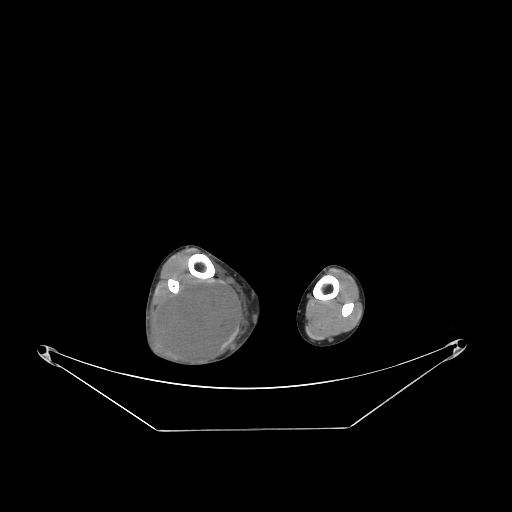
CT of an extremity soft-tissue mass (from a PET/CT study), one axial slice. Slice 71 of 267 in the series (ordered by position). Reconstruction kernel STANDARD. Soft-tissue window (W 400 / L 40 HU). 3.75 mm slice thickness. 512 × 512 image matrix. Male patient. From the clinical record (not read from this slice): histological type: liposarcoma - round cell; grade: high; site of the primary tumour: right calf.
Structures marked on this image (expert contour drawn on MRI and transferred to this co-registered scan by the dataset authors):
- gross tumour volume (mass): bounding box [x1, y1, x2, y2] px = [153, 278, 241, 366]